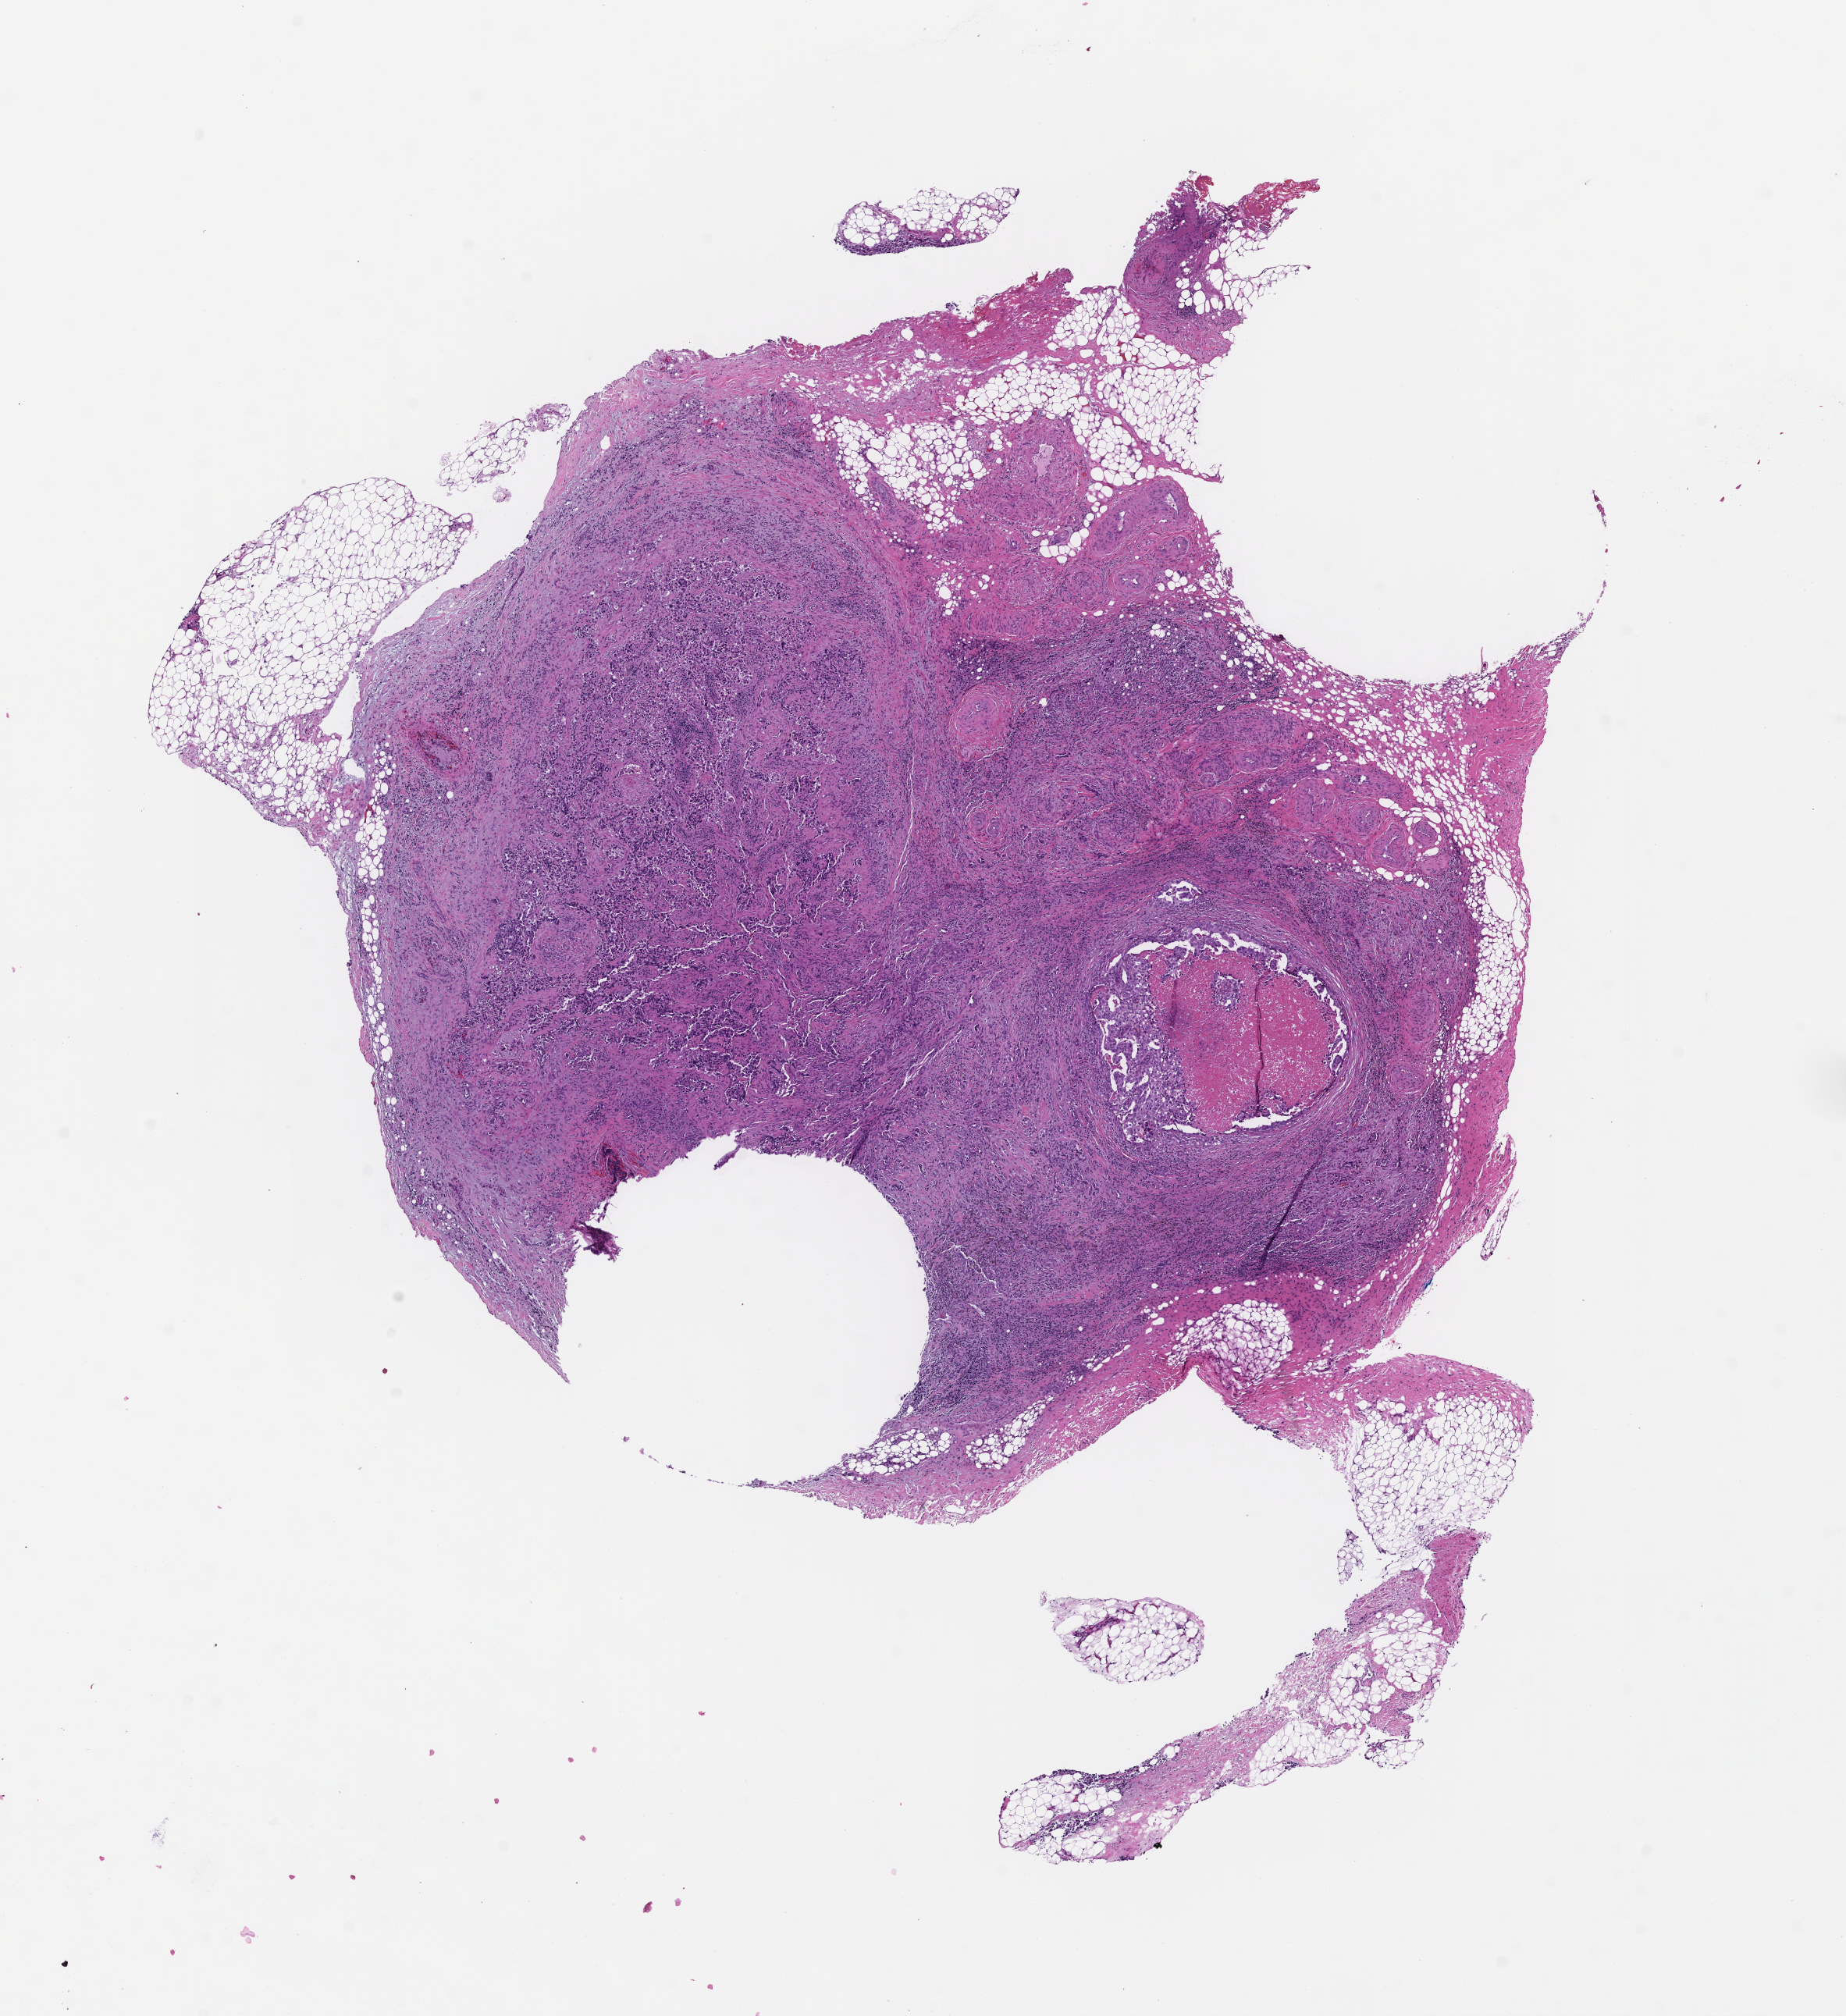
Whole-slide image, H&E stain — whole scanned area (about 9.5 x 10.4 mm) shown as a low-resolution overview. Formalin-fixed paraffin-embedded section. Specimen time point: archival tissue. Patient sex: female.
• this section: metastasis (sampled organ not recorded)
• patient diagnosis (primary): Non-Small Cell Lung Carcinoma